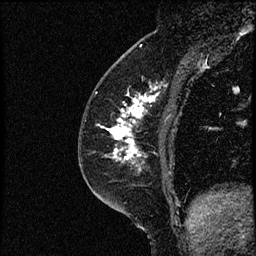
Breast MRI (dynamic contrast-enhanced), one sagittal slice; dynamic contrast-enhanced study with each time point stored as its own series, time point 2 of 3 at this slice position (early post-contrast, ordered by acquisition time); 1.5 T; TE 4.2 ms, TR 17.6 ms; 256 × 256 image matrix, field of view 200 × 200 mm. Female patient, age 49 years. From the clinical record (not read from this slice): setting: breast cancer imaged before/during neoadjuvant chemotherapy; receptor status: HER2-positive.
Annotated regions visible in this slice (semi-automatically segmented with operator editing):
- analysis volume of interest (the breast-tissue region the enhancement analysis was run in; not a lesion): bounding box (x1, y1, x2, y2) in pixels: (85, 65, 182, 175)
- tumour enhancement mask (voxels above the 100 % enhancement threshold inside the analysis volume of interest): (104, 84, 162, 170)